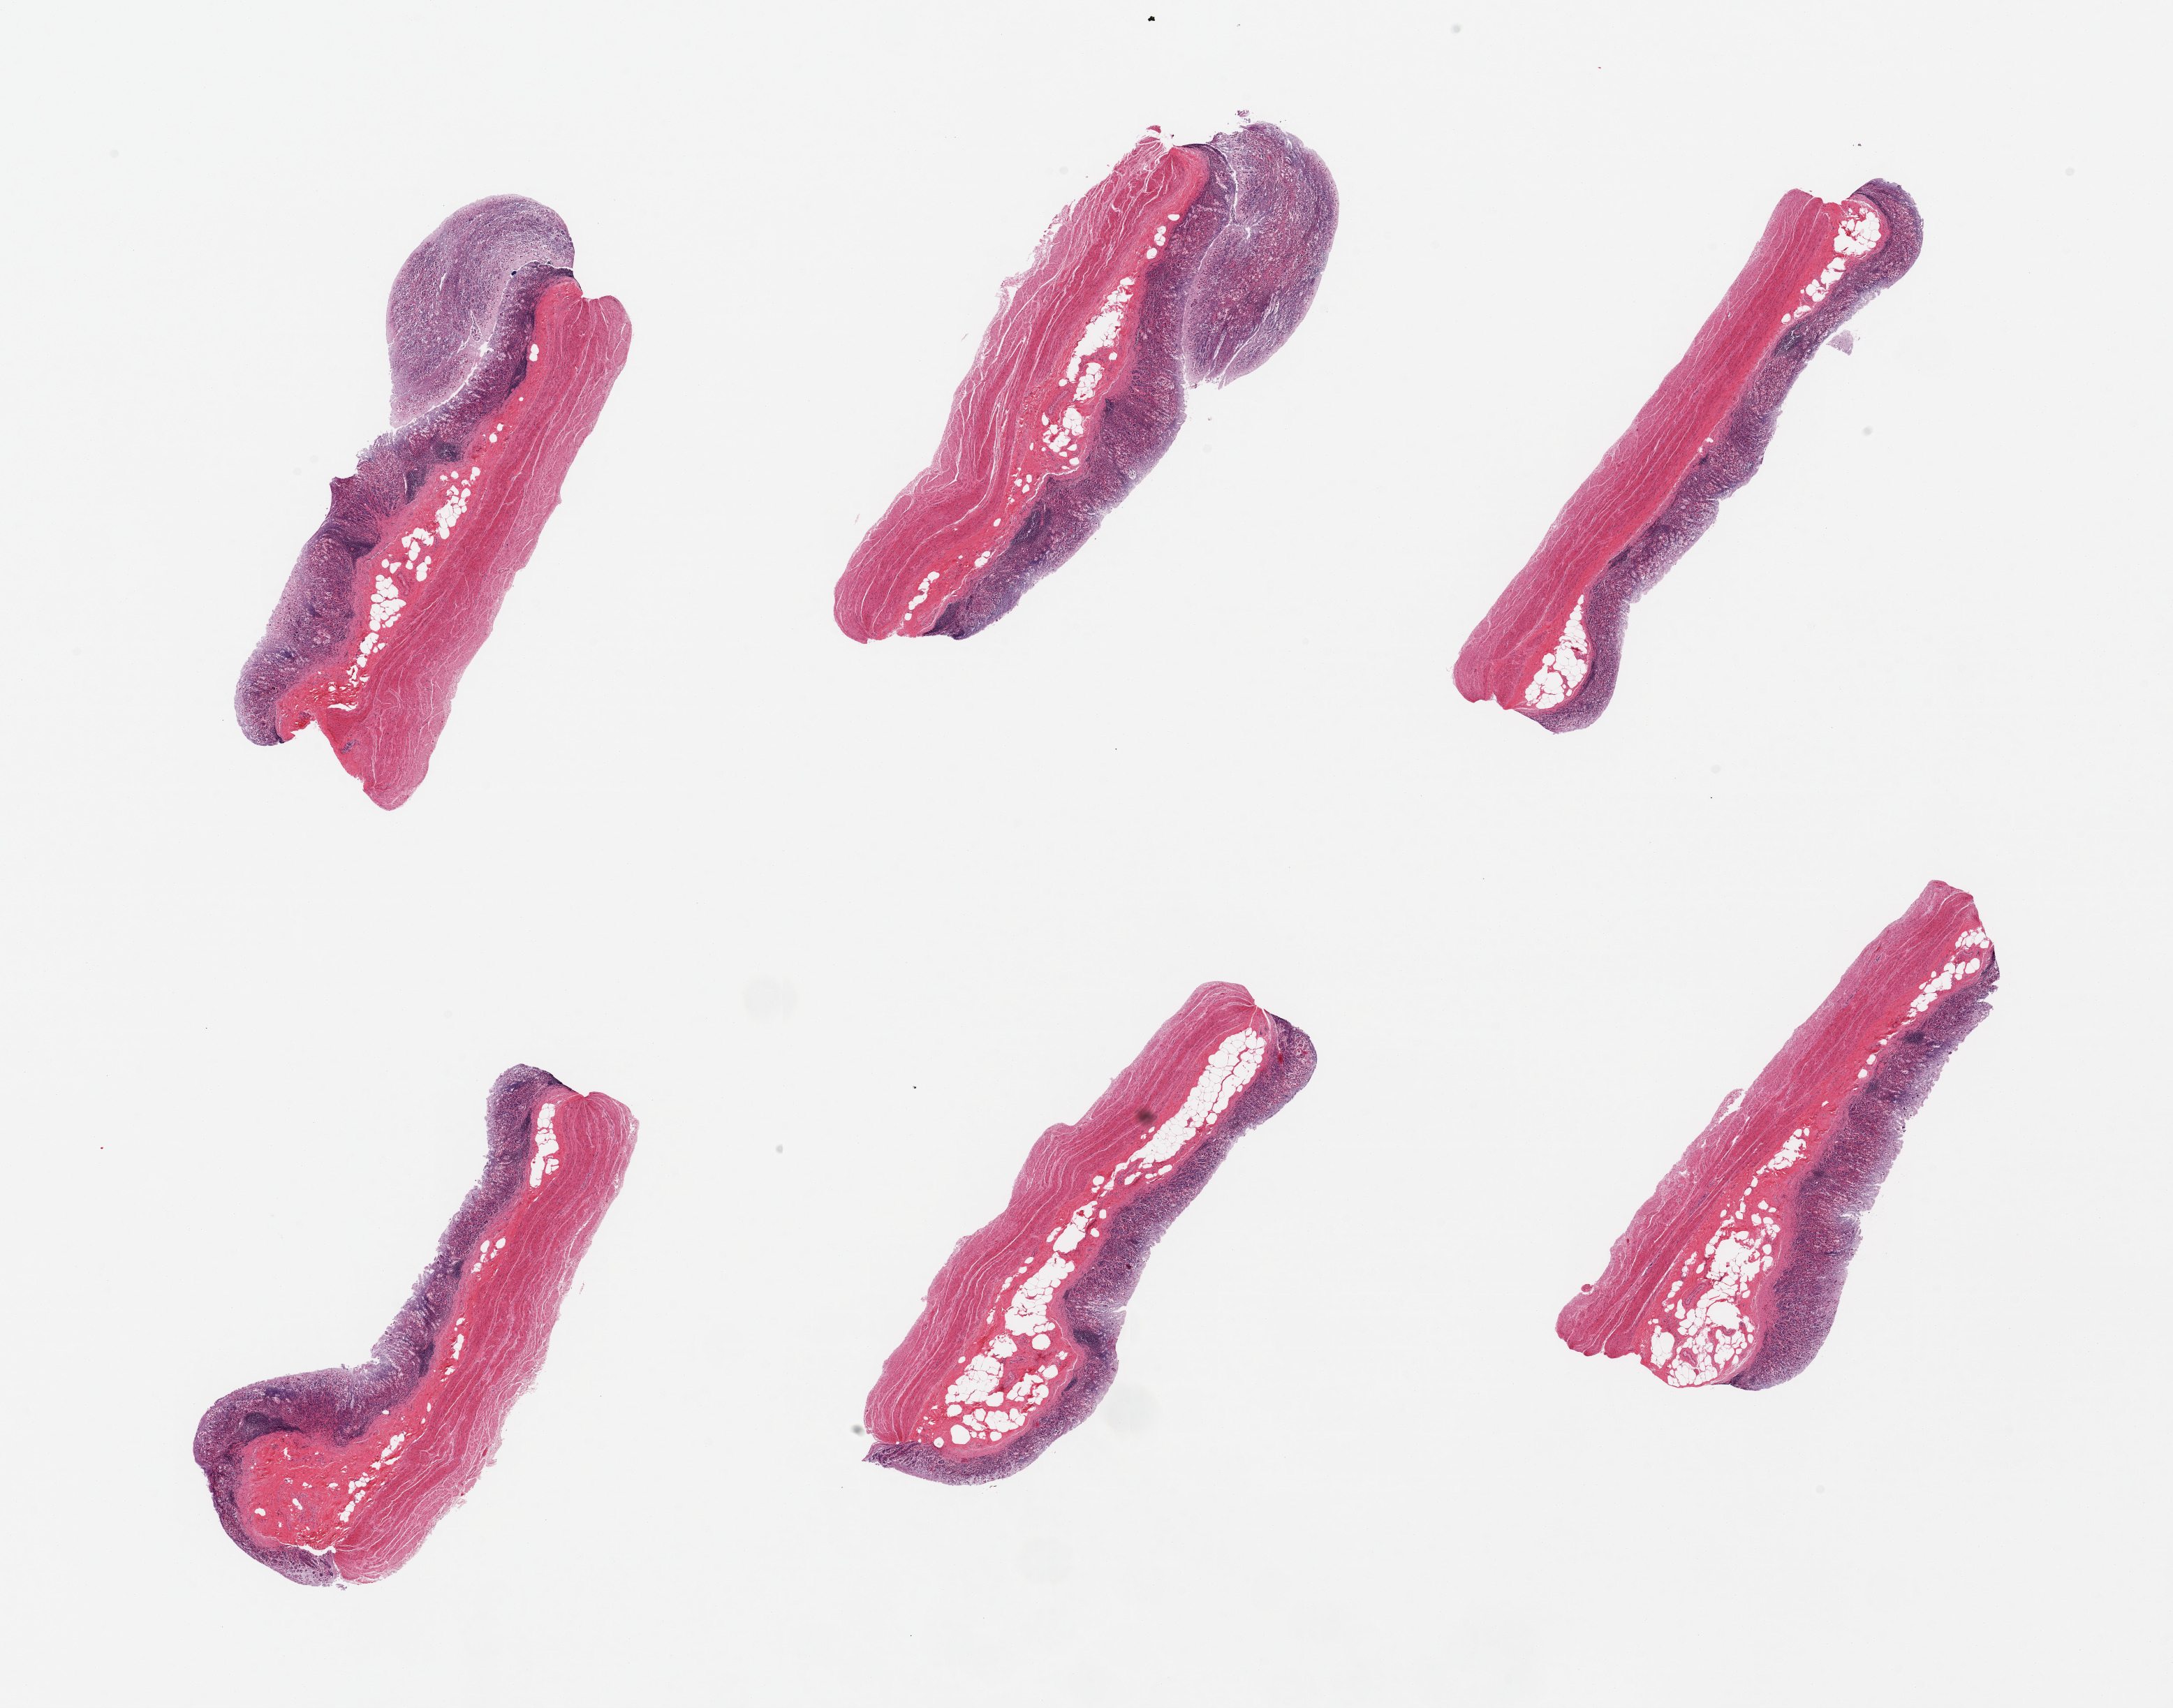
Hematoxylin and eosin (H&E) whole-slide image, whole scanned area (about 24.6 x 19.3 mm, from a 20x scan) shown as a low-resolution overview, PAXgene-fixed, paraffin-embedded tissue, target tissue: stomach, tissue donor sample. Female donor.
* pathologist's review note for this sample: 6 pieces, mucosa up to ~0.5mm but with advanced autolysis focally, moderate over all